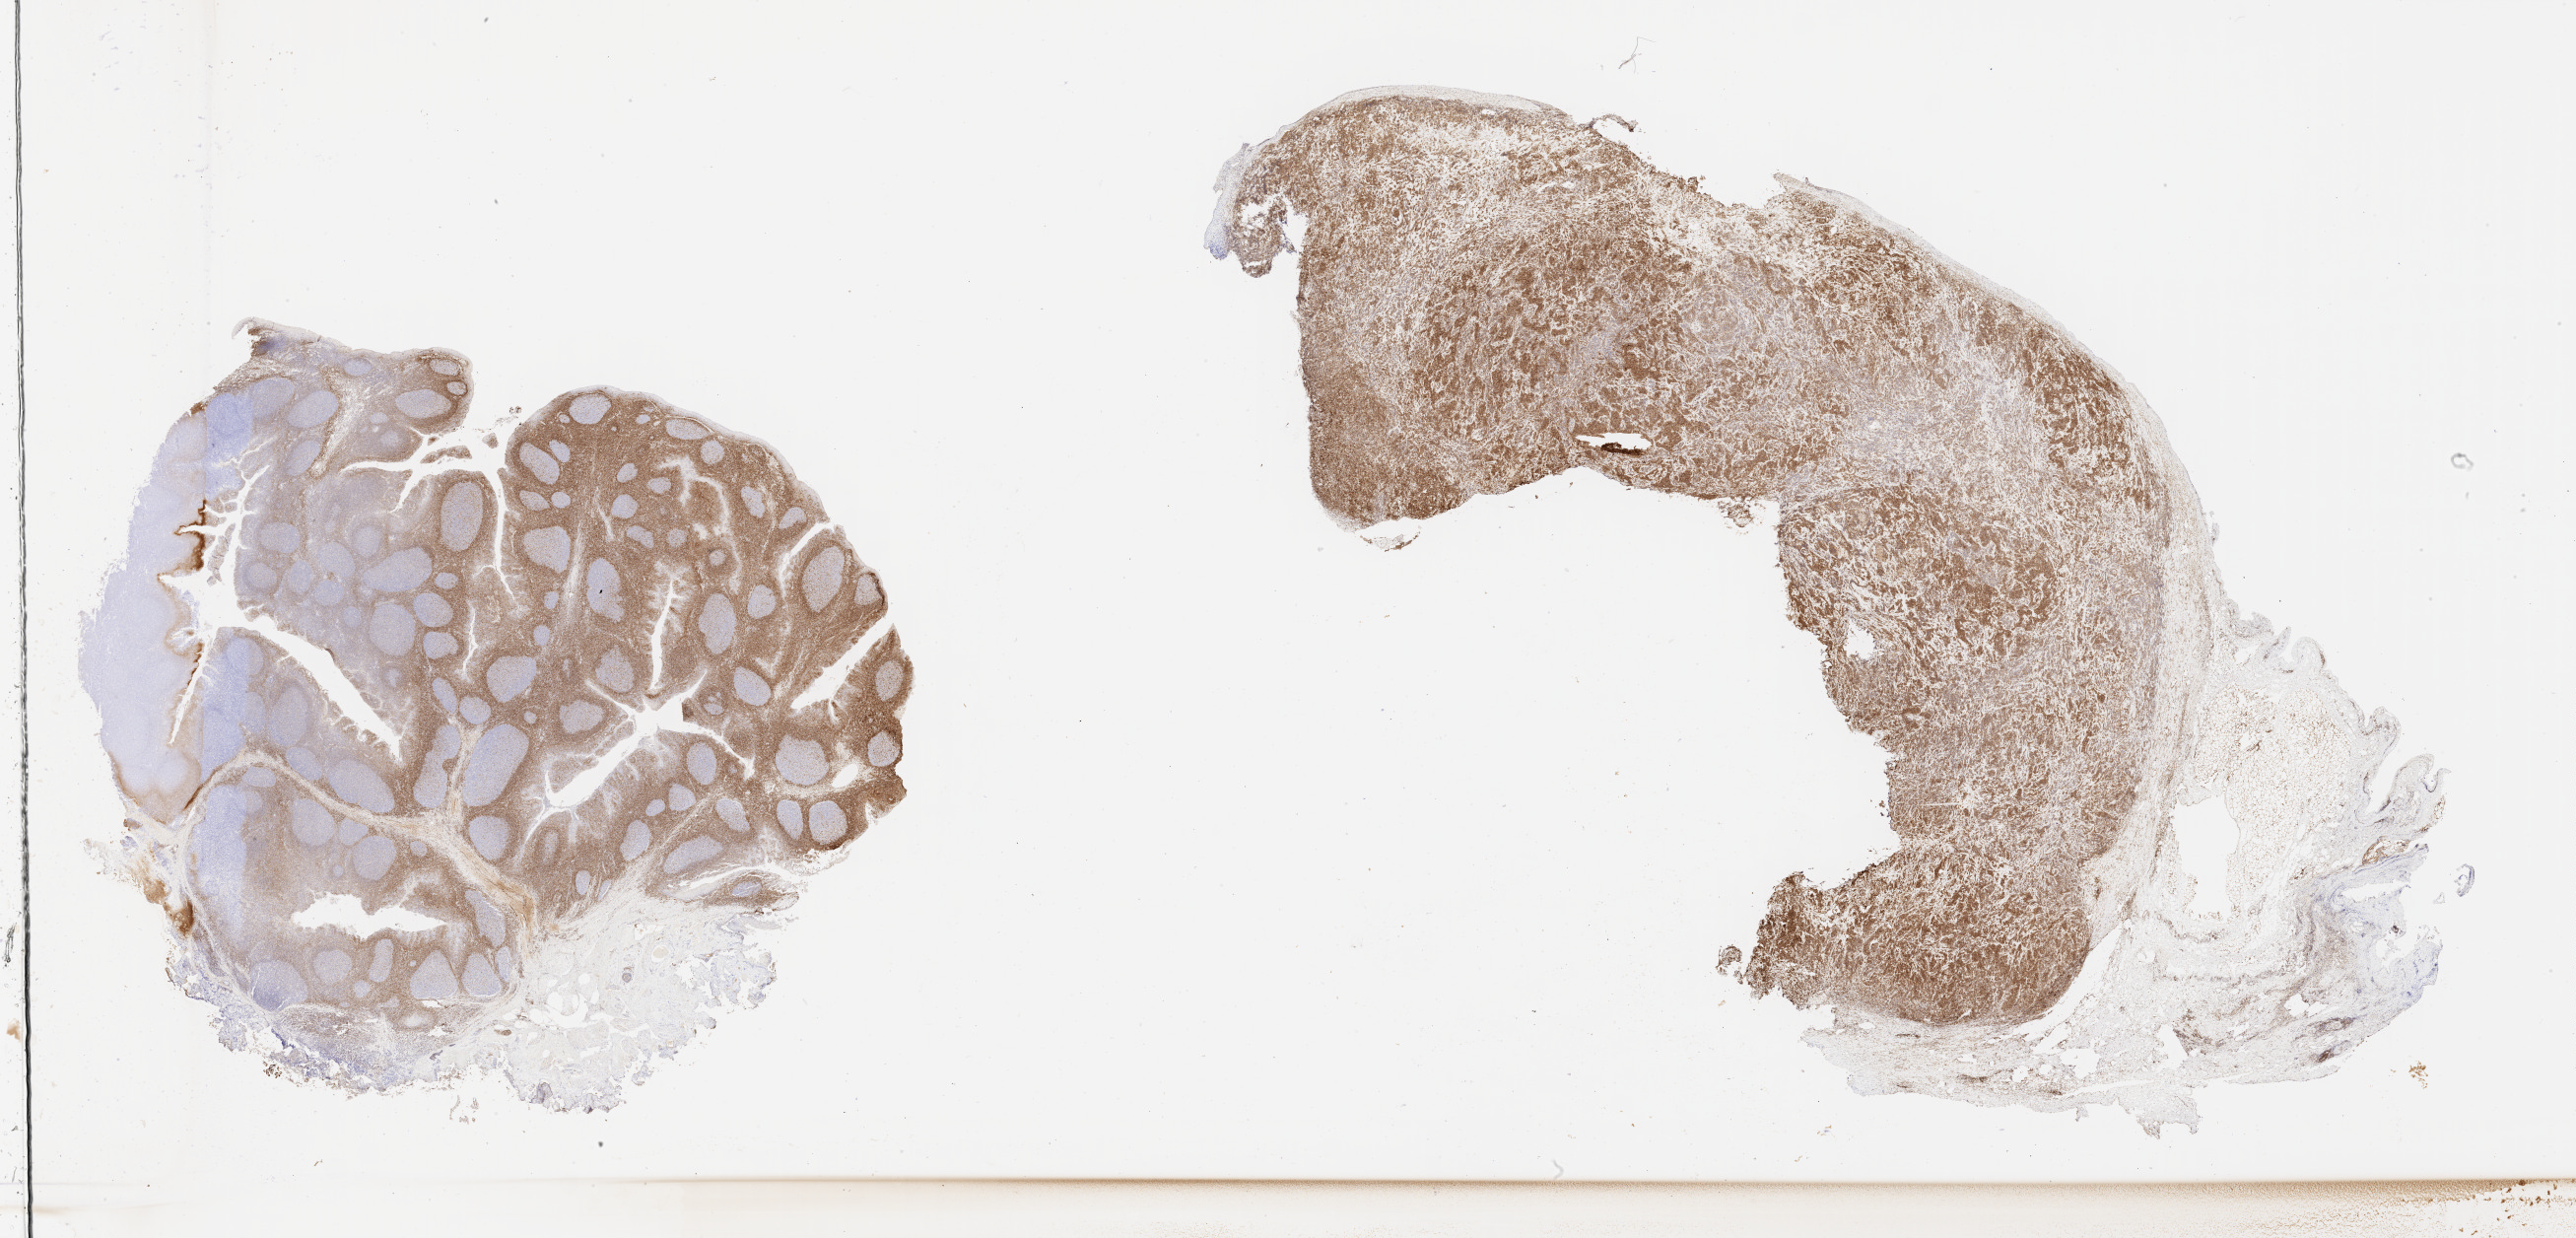
Immunohistochemistry (IHC) whole-slide image stained for BCL2 — low-resolution overview of the scanned area, about 42.3 x 20.3 mm, tumor tissue, site: bone. Patient male; age 48 years.
Diagnosis: Diffuse large B-cell lymphoma, NOS.